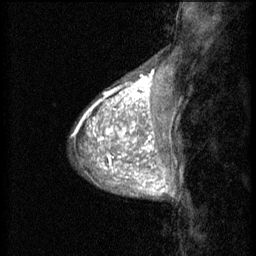
Breast MRI (dynamic contrast-enhanced), one sagittal slice. Slice 14 of 60 in the series (ordered by position). 3 images stored at this slice position (order not interpretable as contrast timing). 1.5 T. TE 4.2 ms, TR 8.2 ms. 2 mm slice thickness. 256 × 256 image matrix, field of view 180 × 180 mm. Female patient, age 38 years.
Outlined on this slice (semi-automatically segmented with operator editing):
- analysis volume of interest (the breast-tissue region the enhancement analysis was run in; not a lesion): box from (x=95, y=106) to (x=157, y=171) px
- tumour enhancement mask (voxels above the 70 % enhancement threshold inside the analysis volume of interest): (x=95, y=106)–(x=157, y=171)